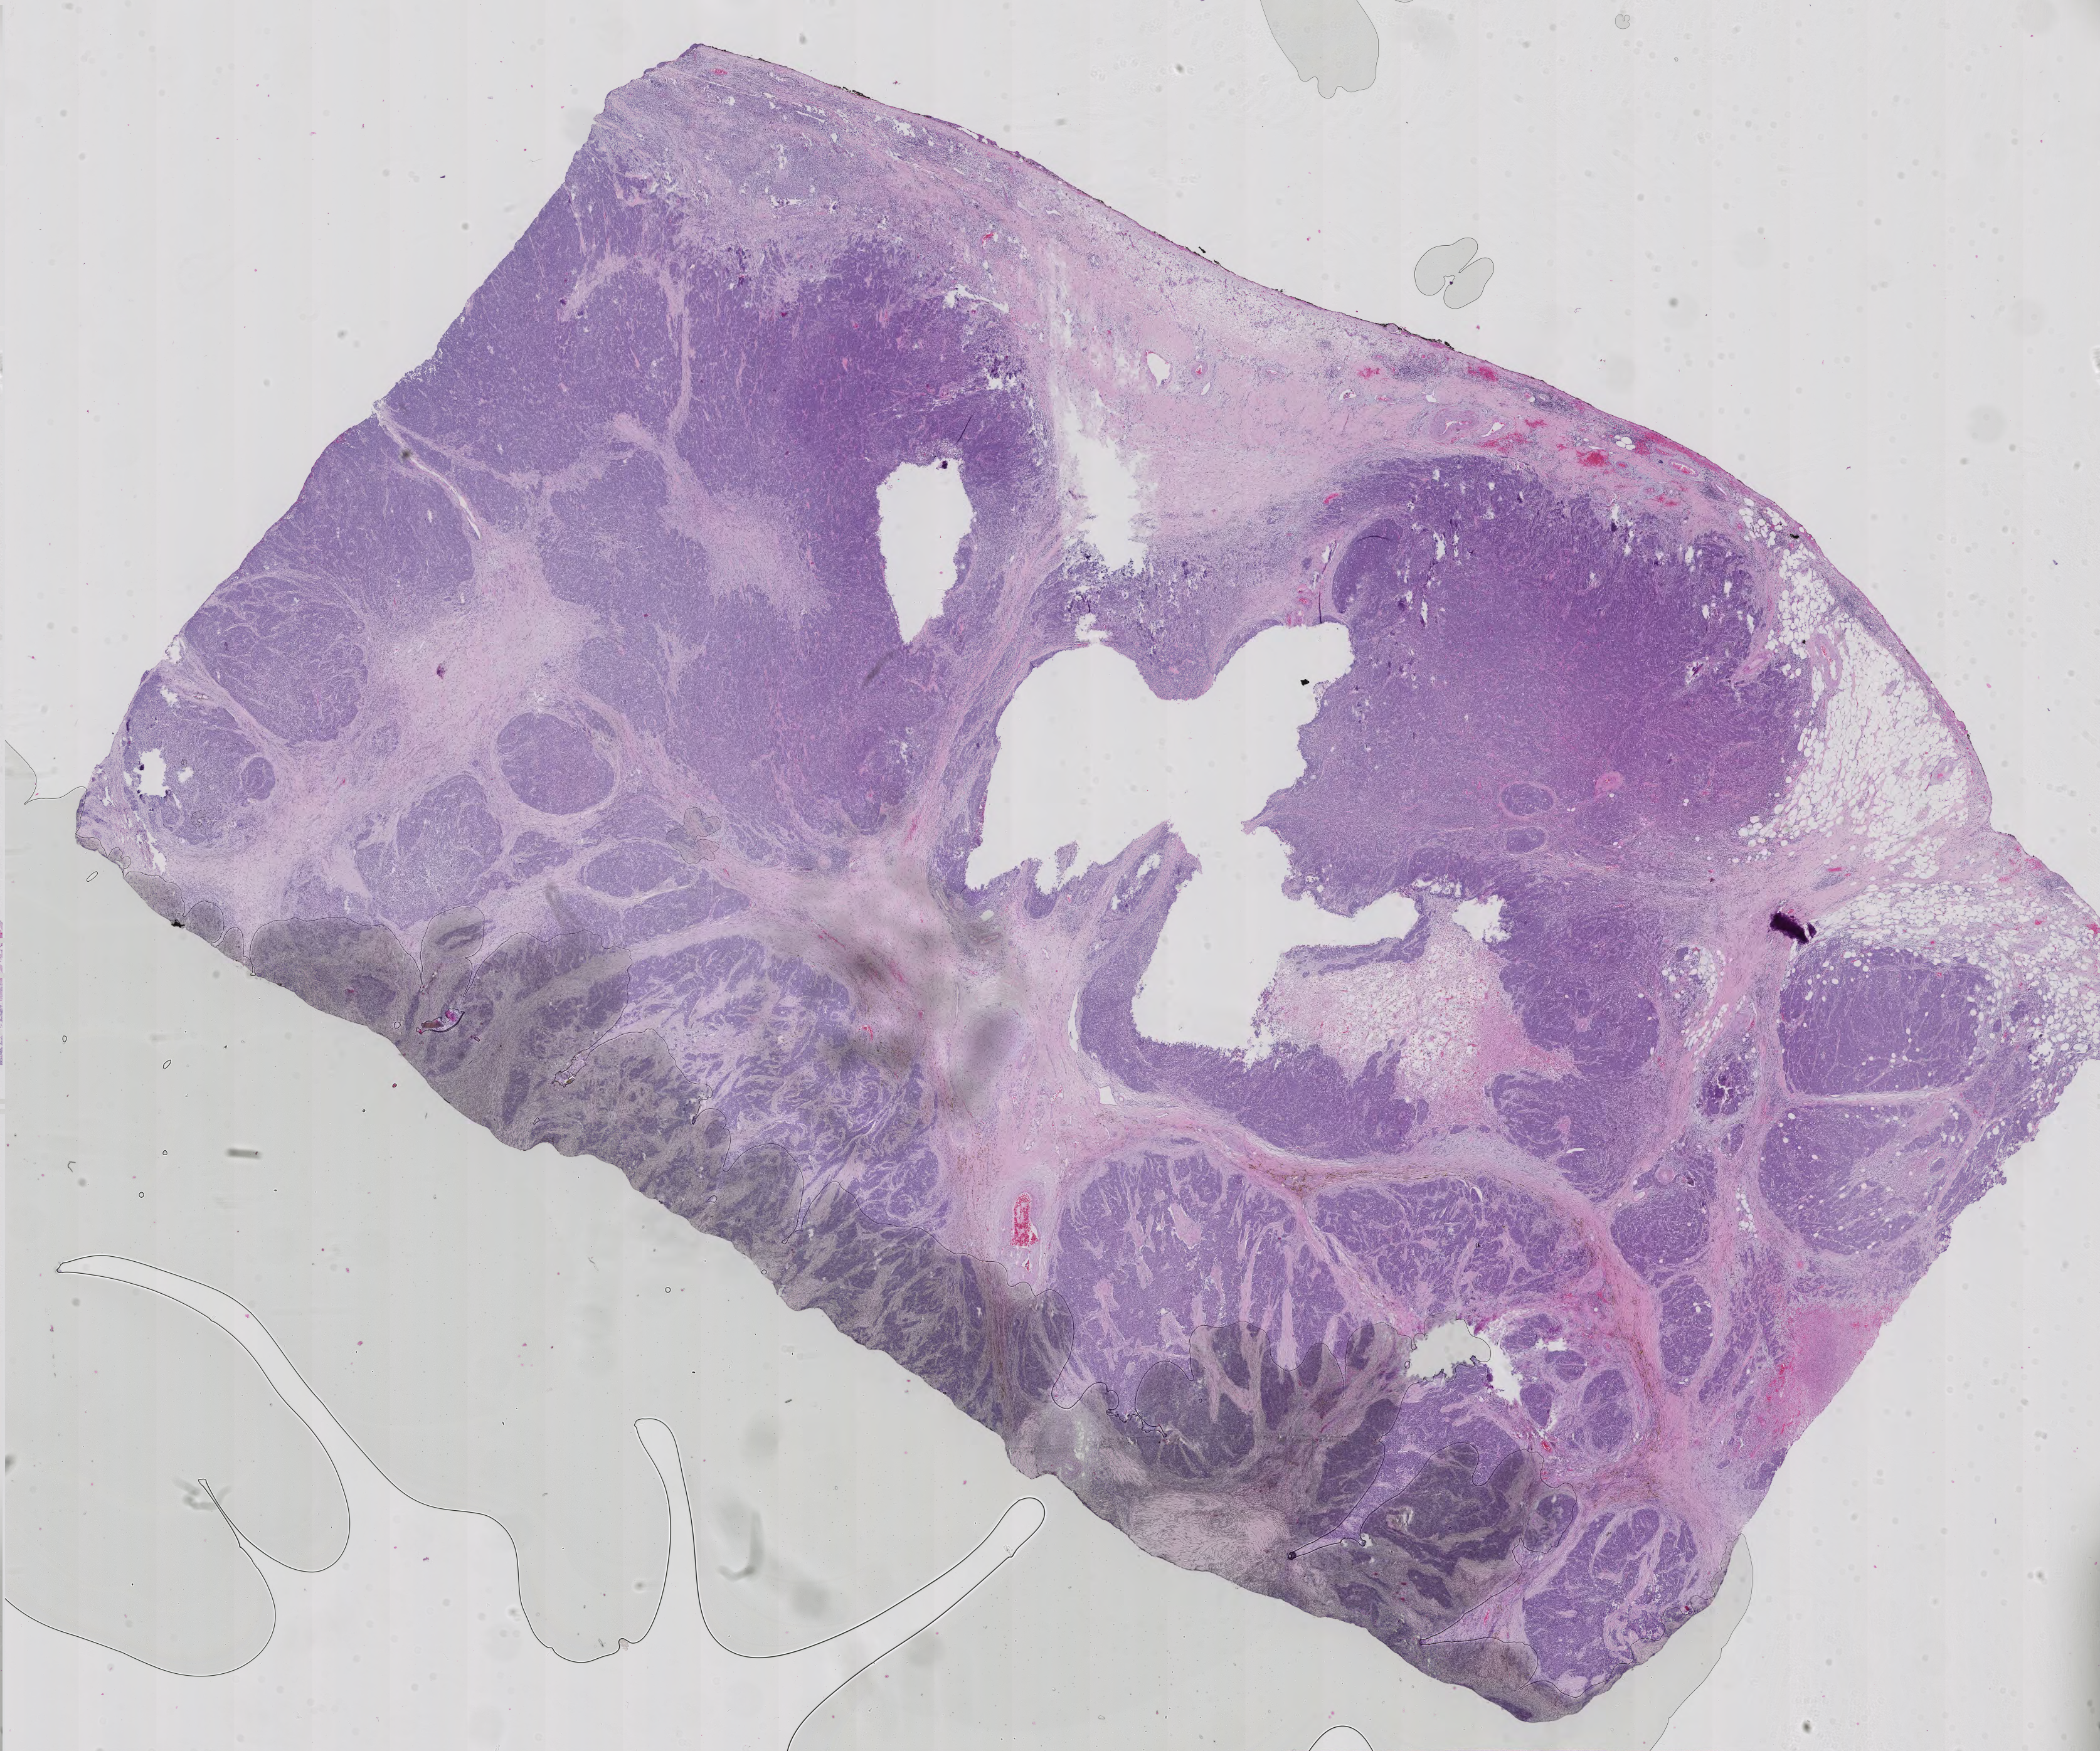
Whole-slide histology image, H&E-stained — whole scanned area (about 24.4 x 20.4 mm) shown as a low-resolution overview; formalin-fixed paraffin-embedded (FFPE) diagnostic section; primary tumour sample from the thymus. Female, age 78 years at initial diagnosis.
- diagnosis: Thymic carcinoma, NOS